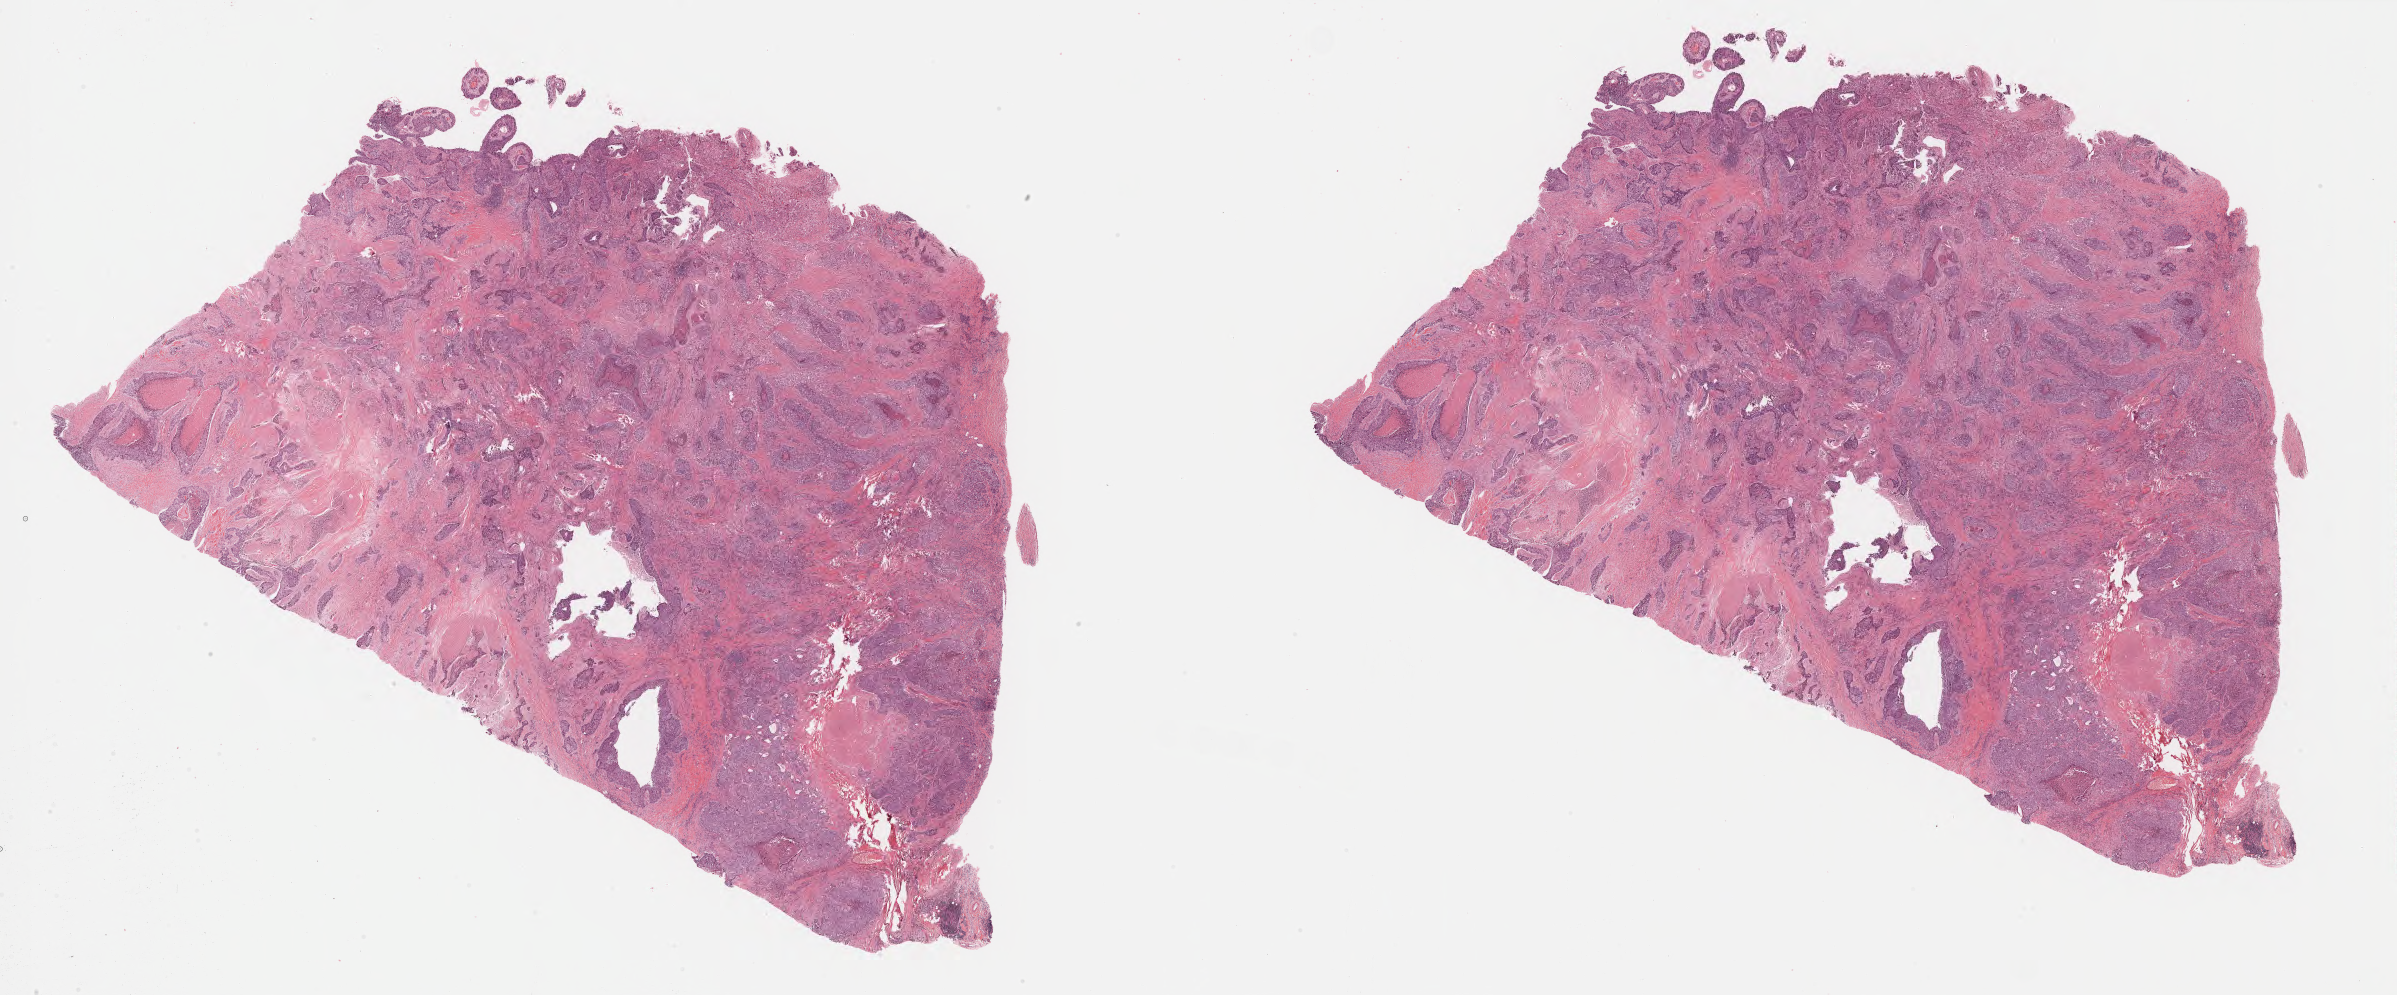
Digitized Hematoxylin and eosin (H&E) stained tissue section (whole slide) — whole scanned area (about 38.7 x 16.1 mm, slide scanned at 40x) shown as a low-resolution overview, FFPE section, primary tumour sample from the lung. Patient: male, age at initial diagnosis 57 years.
Diagnosis: Squamous cell carcinoma, NOS (lower lobe, lung). AJCC pathologic stage: IIIA.